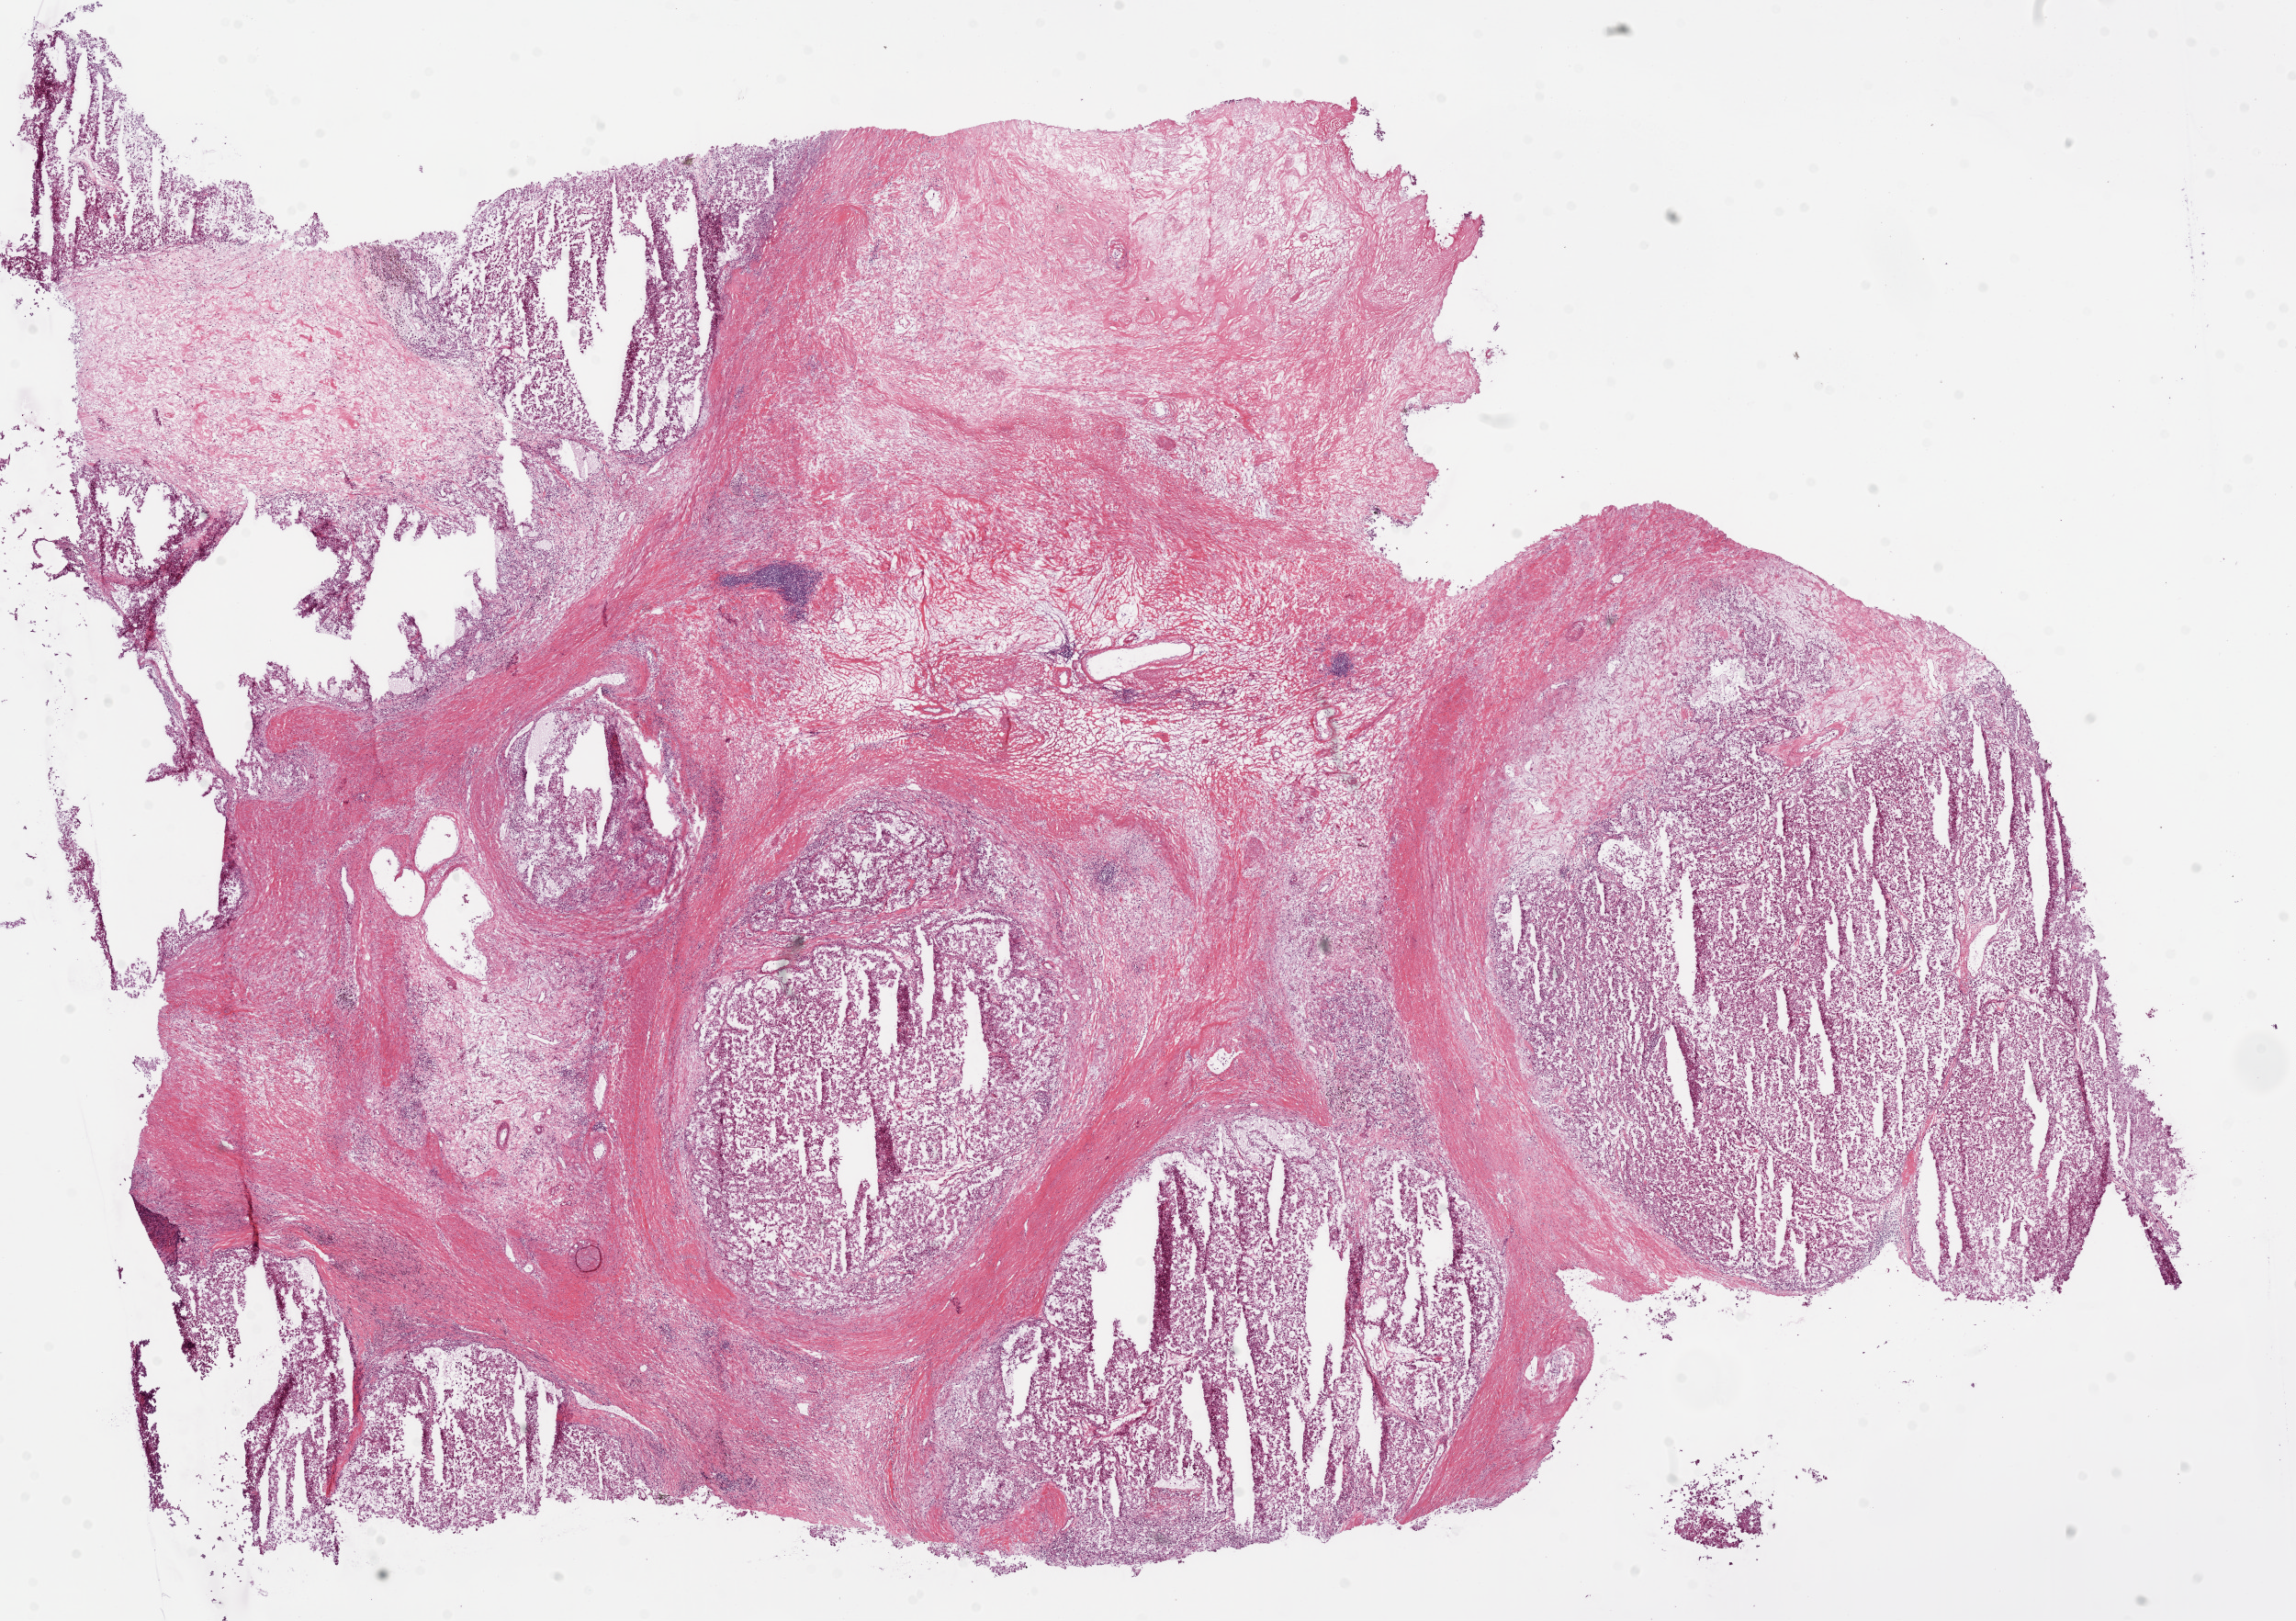
Whole-slide histology image, H&E-stained, shown as a low-resolution overview of the whole scanned area (about 20.1 x 14.2 mm, acquisition: 20x scan), frozen section, sample: primary tumour, kidney. Male, age 58 years at initial diagnosis. Histologic grade: G2 (moderately differentiated). Pathologist review of this section (percent, as recorded): tumour cells 65%, tumour nuclei 80%, normal cells 0%, stromal cells 35%, necrosis 0%.
* AJCC pathologic stage: II
* diagnosis: Clear cell adenocarcinoma, NOS
* laterality: left